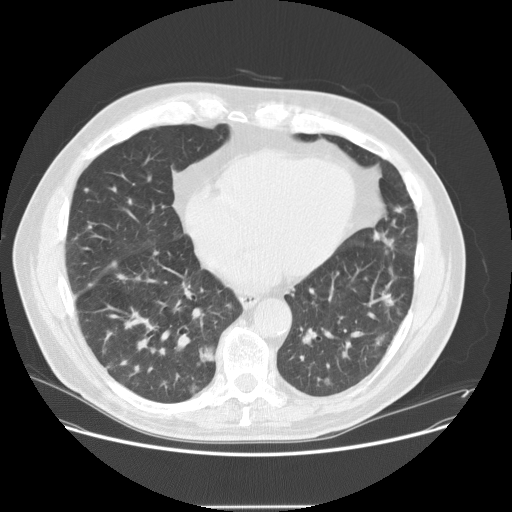
Low-dose screening chest CT, one axial slice; slice 56 of 143 in the series (ordered by position); 120 kVp; lung window (W 1500 / L -600 HU); 2.5 mm slice thickness; 512 × 512 image matrix, field of view 400 × 400 mm.
Structures marked on this image (expert manual segmentation):
- lesion 1 (tumor, lower lobe of right lung): bounding box [x1, y1, x2, y2] px = [203, 347, 215, 362]